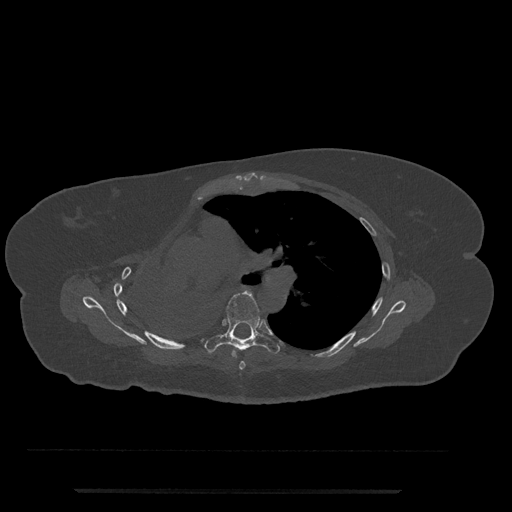
CT including the spine, one axial slice. Position 503 of 797 along the scan axis. Reconstruction kernel Br40s/3. Bone window (W 1800 / L 400 HU). 0.5 mm slice thickness. 512 × 512 image matrix, field of view 440 × 440 mm. Patient: female, 51 years. From the clinical record (not read from this slice): primary cancer: neuro; vertebrae with lytic lesions (as recorded): T8.
Outlined on this slice (semi-automatic segmentation, software-assisted and operator-edited):
- T5 vertebra: bounding box <239,361,246,370> (left, top, right, bottom; pixels)
- T6 vertebra: <206,292,280,359>